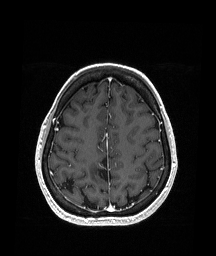
Brain MRI from a brain-tumour surgery series, one axial slice; slice 60 of 151 in the series (ordered by position); T1-weighted post-contrast; 216 × 256 image matrix, field of view 211 × 250 mm. Case-level facts recorded for this patient, not image findings: histopathology: Oligodendroglioma; WHO grade: 2.
Structures marked on this image (manually delineated by an expert):
- previous resection cavity: box from (x=94, y=153) to (x=109, y=183) px